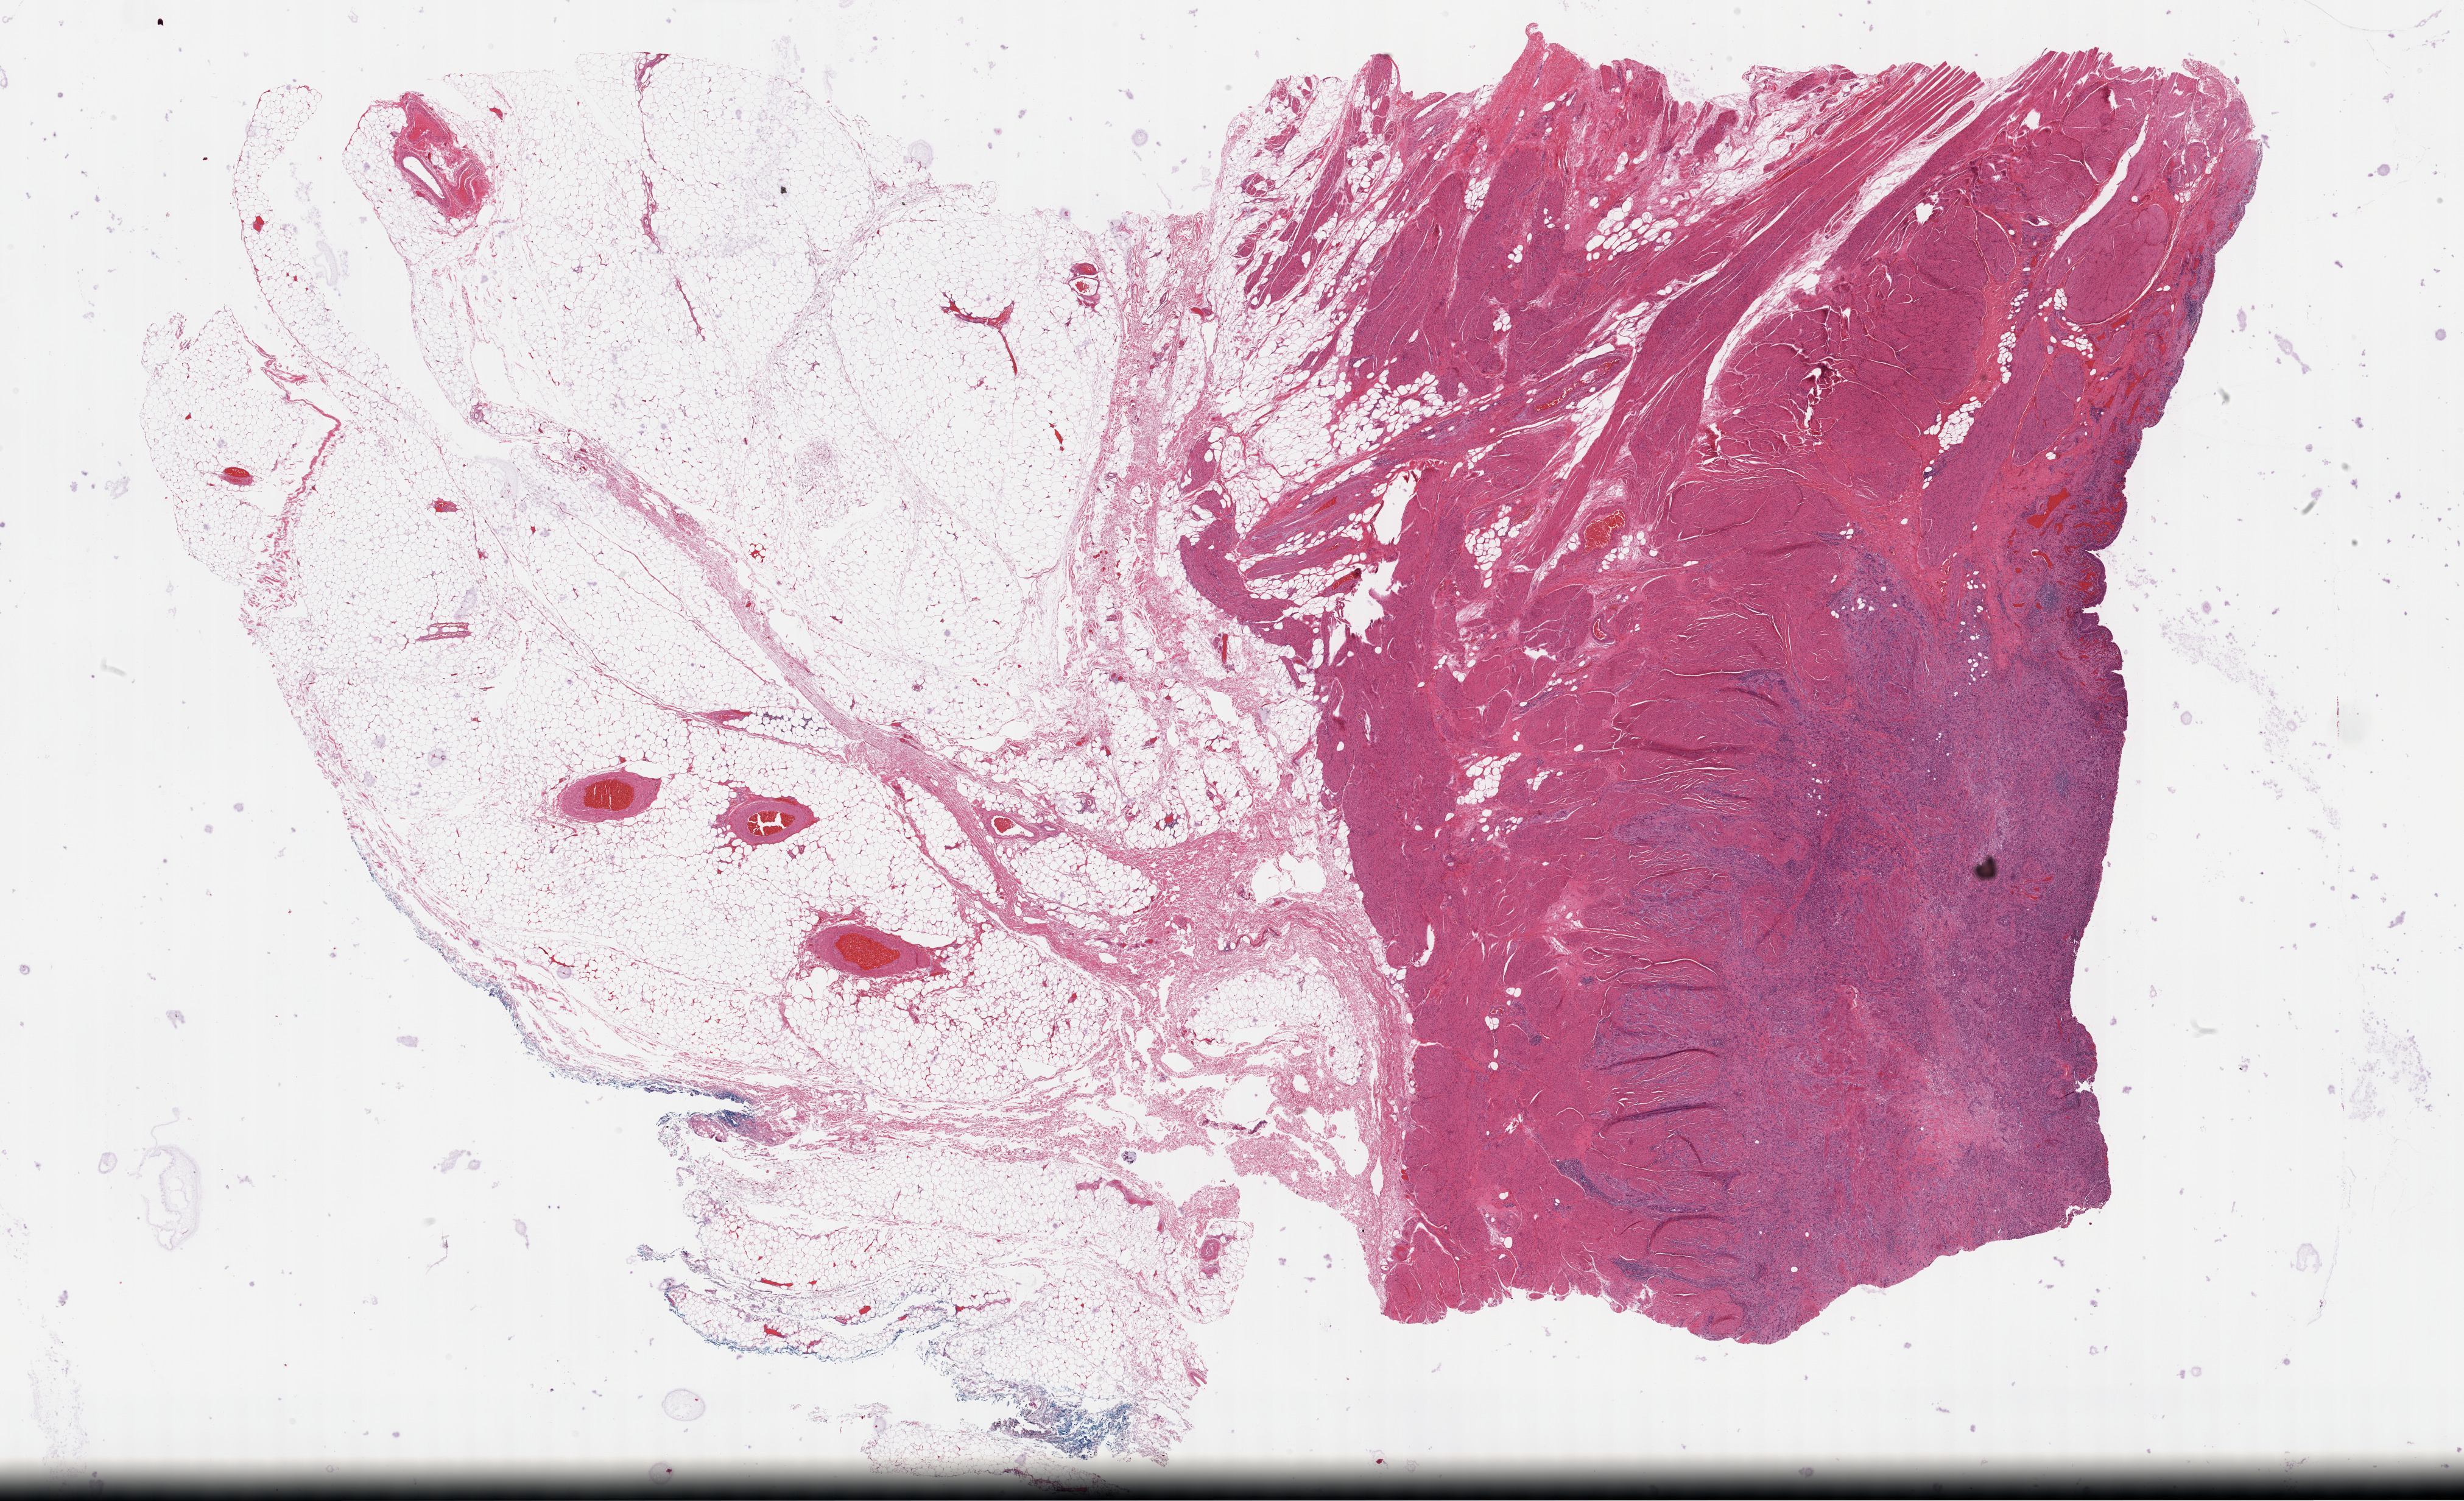
H&E-stained whole-slide image, low-resolution overview of the scanned area, about 32.7 x 19.9 mm (slide scanned at 40x), formalin-fixed paraffin-embedded (FFPE) diagnostic section, sample: primary tumour, bladder. Male, age 60 years at initial diagnosis. Histologic grade: high grade.
Lymph nodes positive (case pathology): 0 of 25 examined. Histologic diagnosis: Transitional cell carcinoma (anterior wall of bladder). TNM: T3a N0 MX. AJCC pathologic stage: III (7th edition).